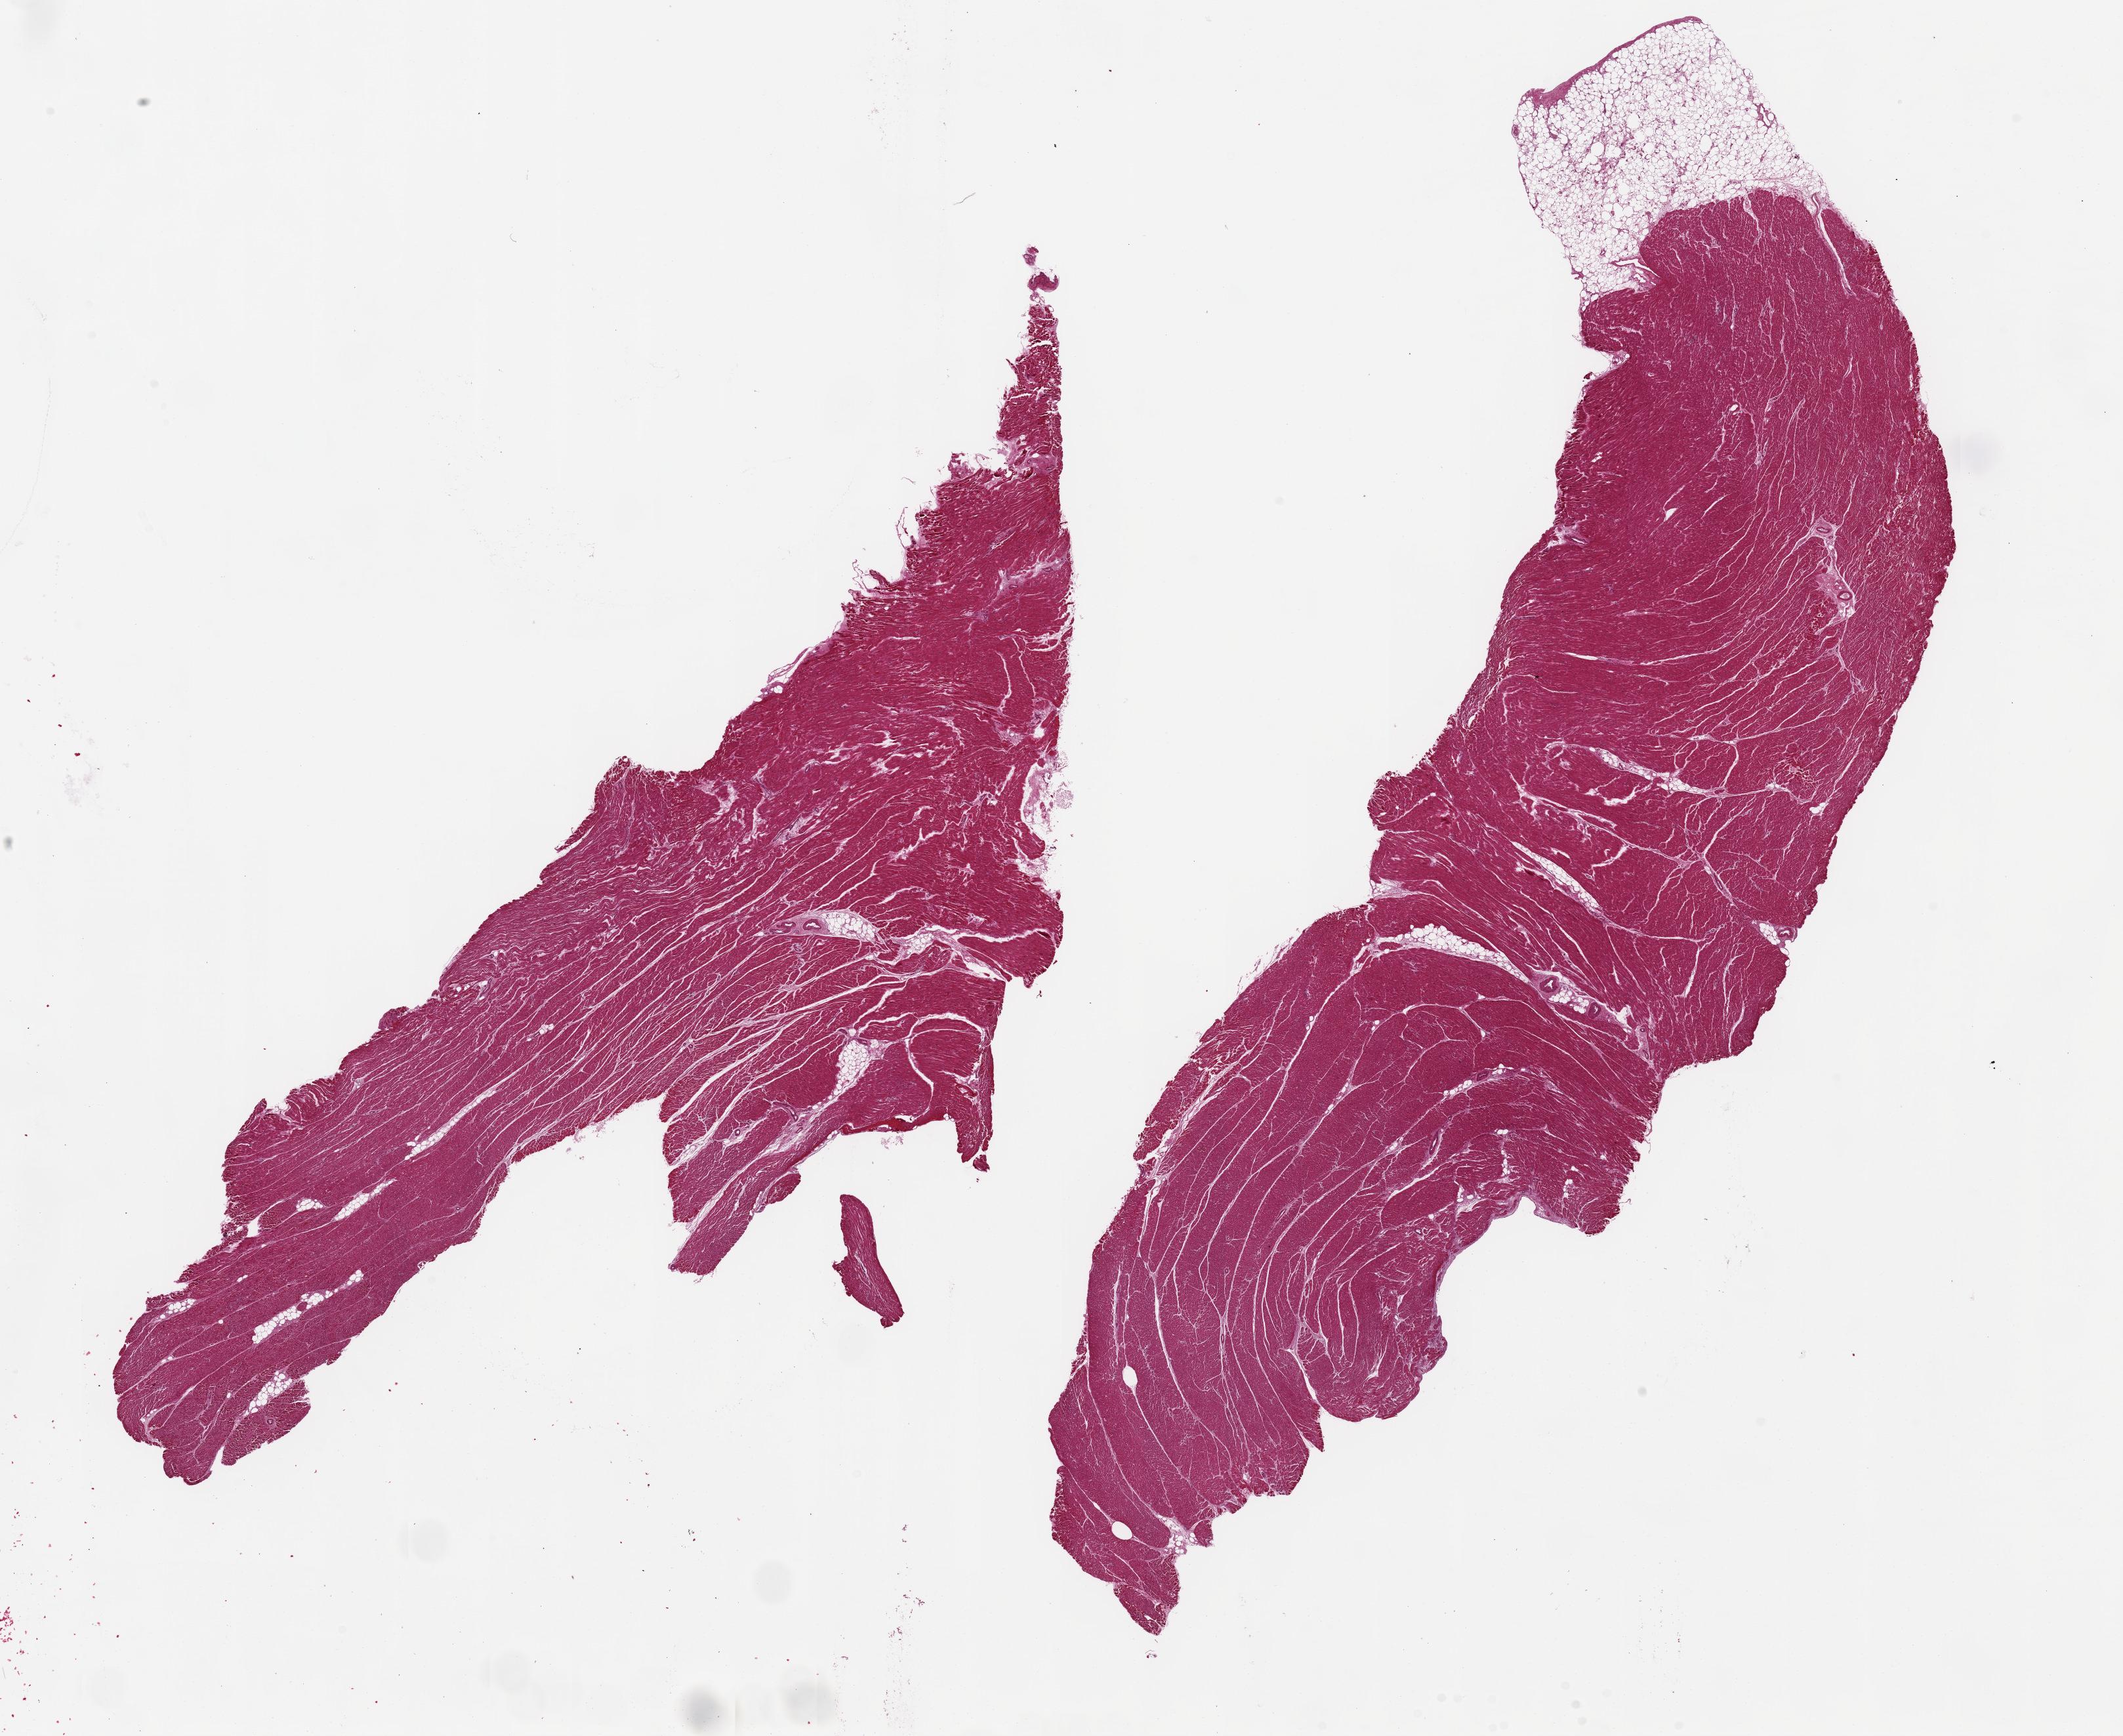
Whole-slide image, haematoxylin and eosin stain — whole scanned area (about 25.6 x 20.9 mm, acquisition: 20x scan) shown as a low-resolution overview. PAXgene-fixed paraffin-embedded (PFPE) section. Section of heart (target tissue). Donor tissue sample. Donor: male.
Reviewer comment on this tissue sample: 2 pieces, 18x13 & 21.5x6mm; hypertrophic fibers; 2 mm adipose at one end of 1 piece.